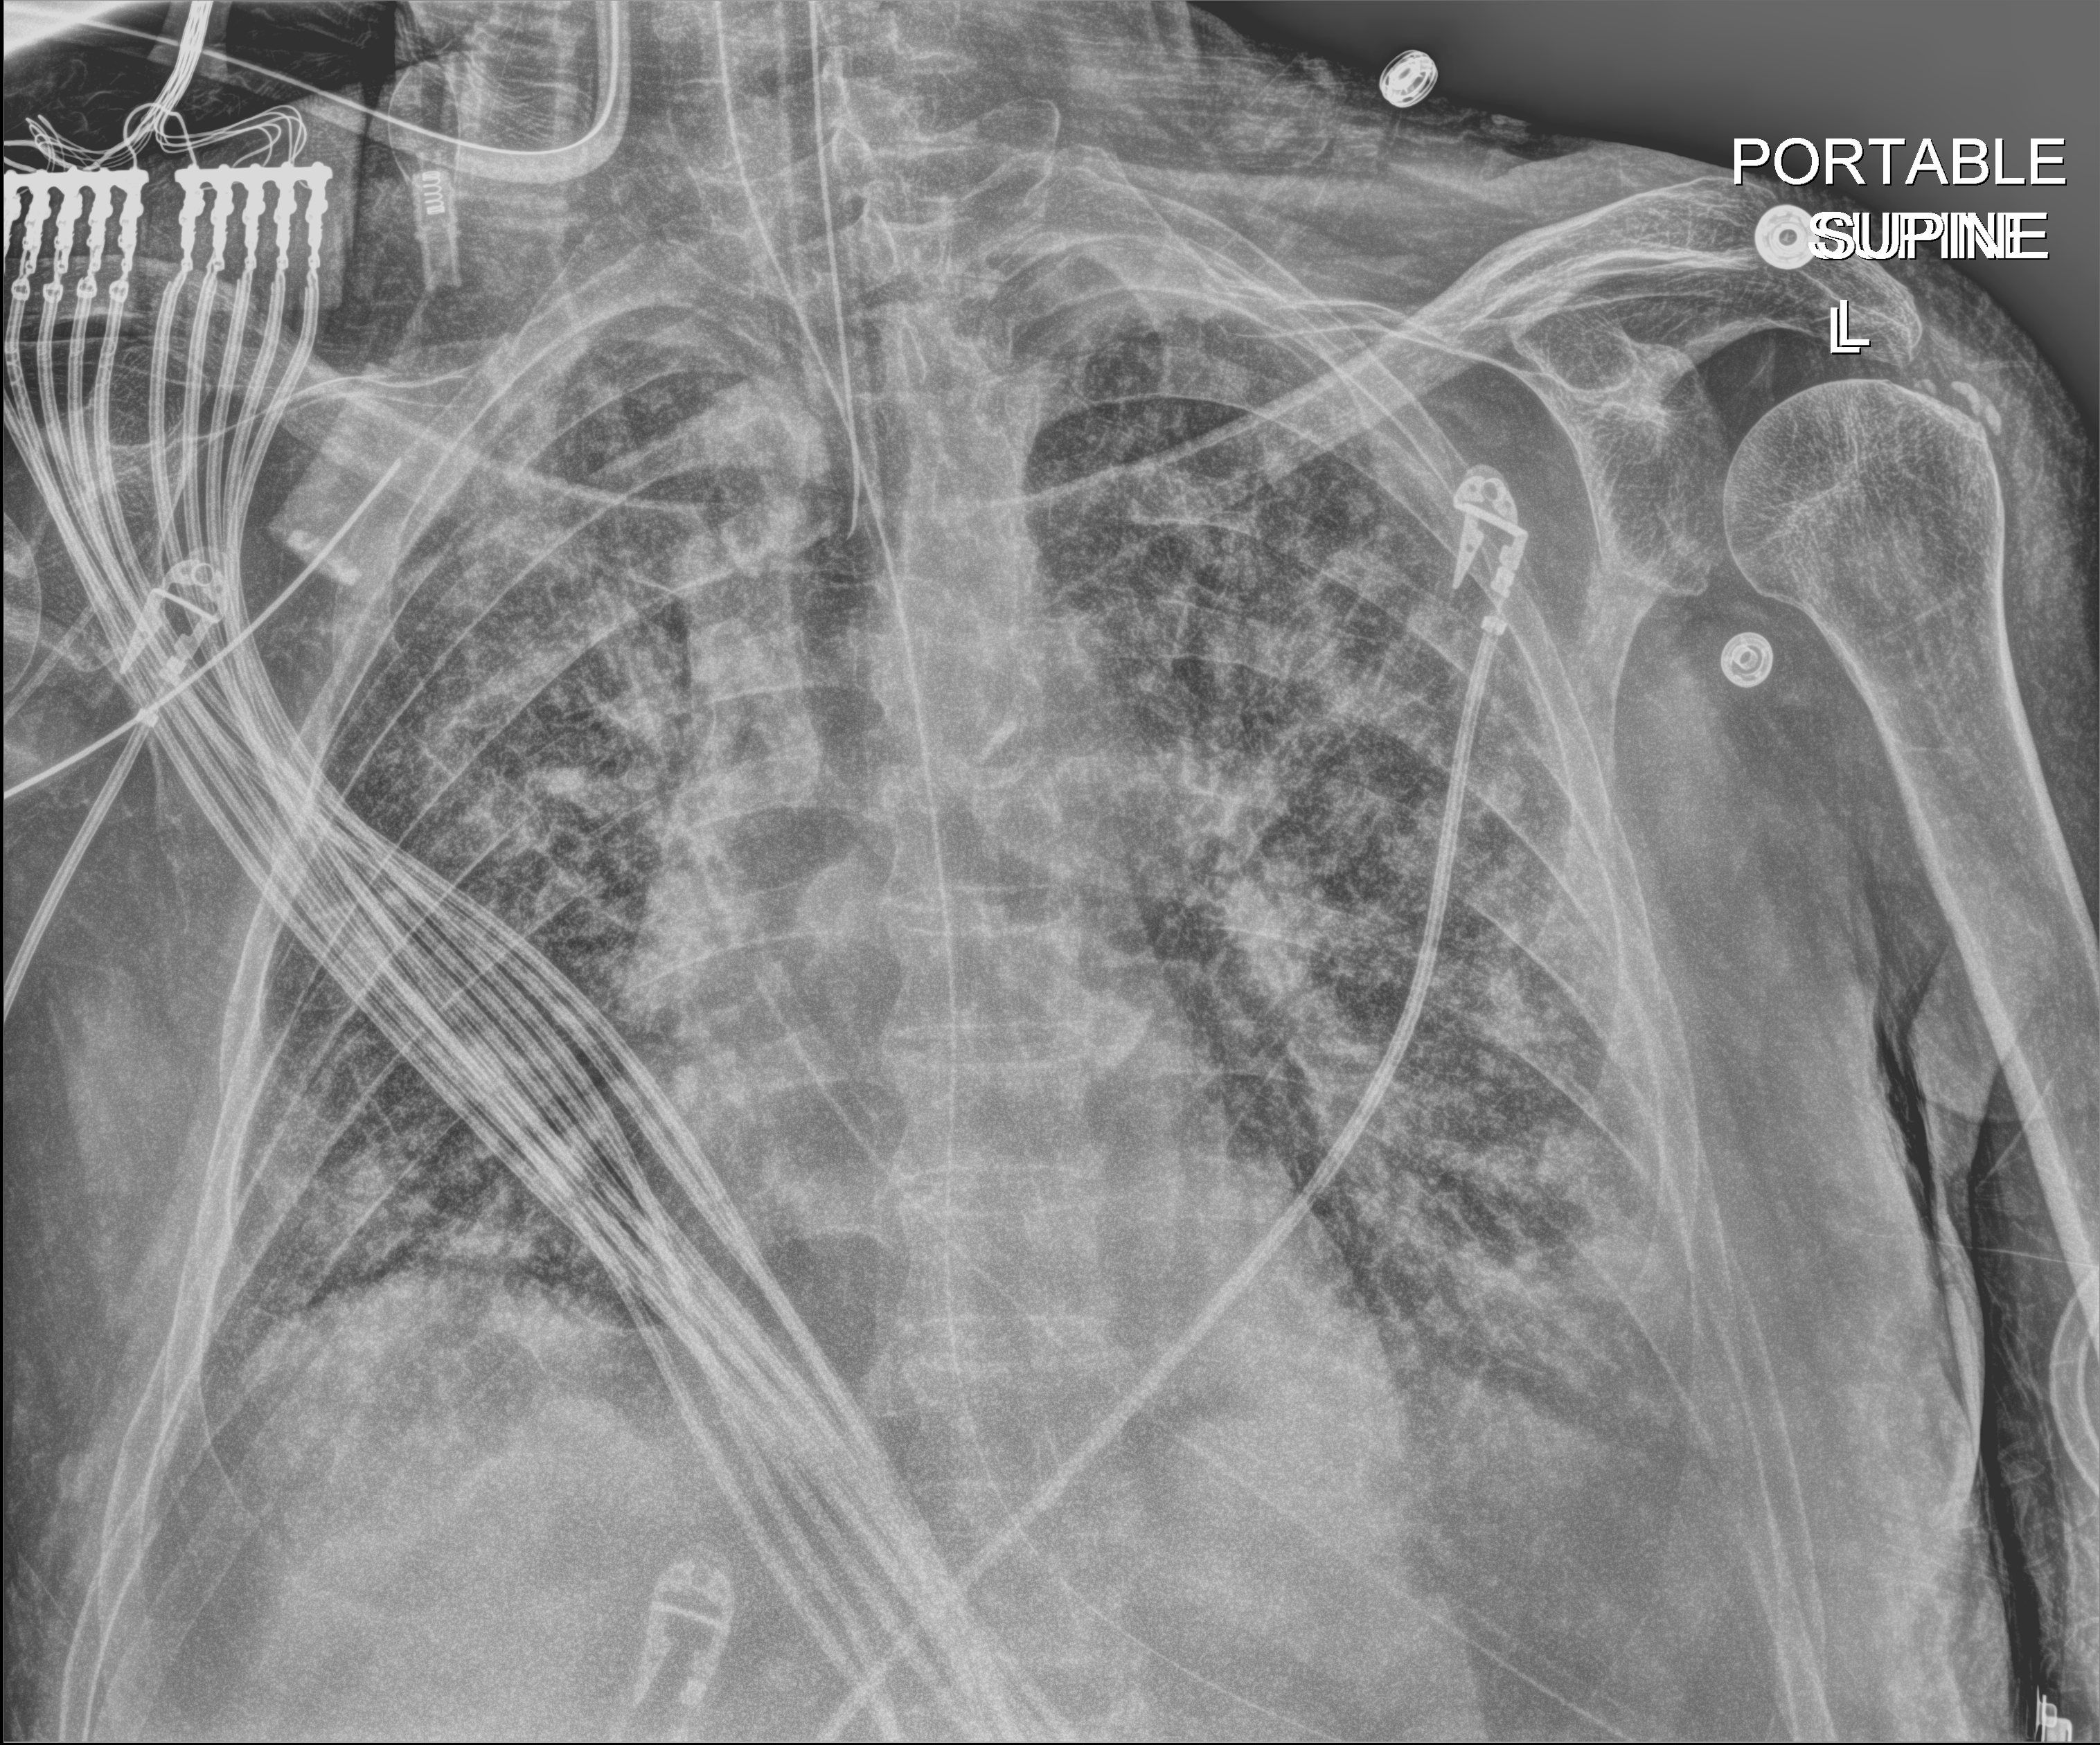
Chest X-ray, anteroposterior (AP) projection. Male patient hospitalised with COVID-19, age 60–74 years.
Hospital-stay facts (about this admission, not read from this image; timing relative to this image not recorded): admitted to intensive care during this hospital stay: yes.